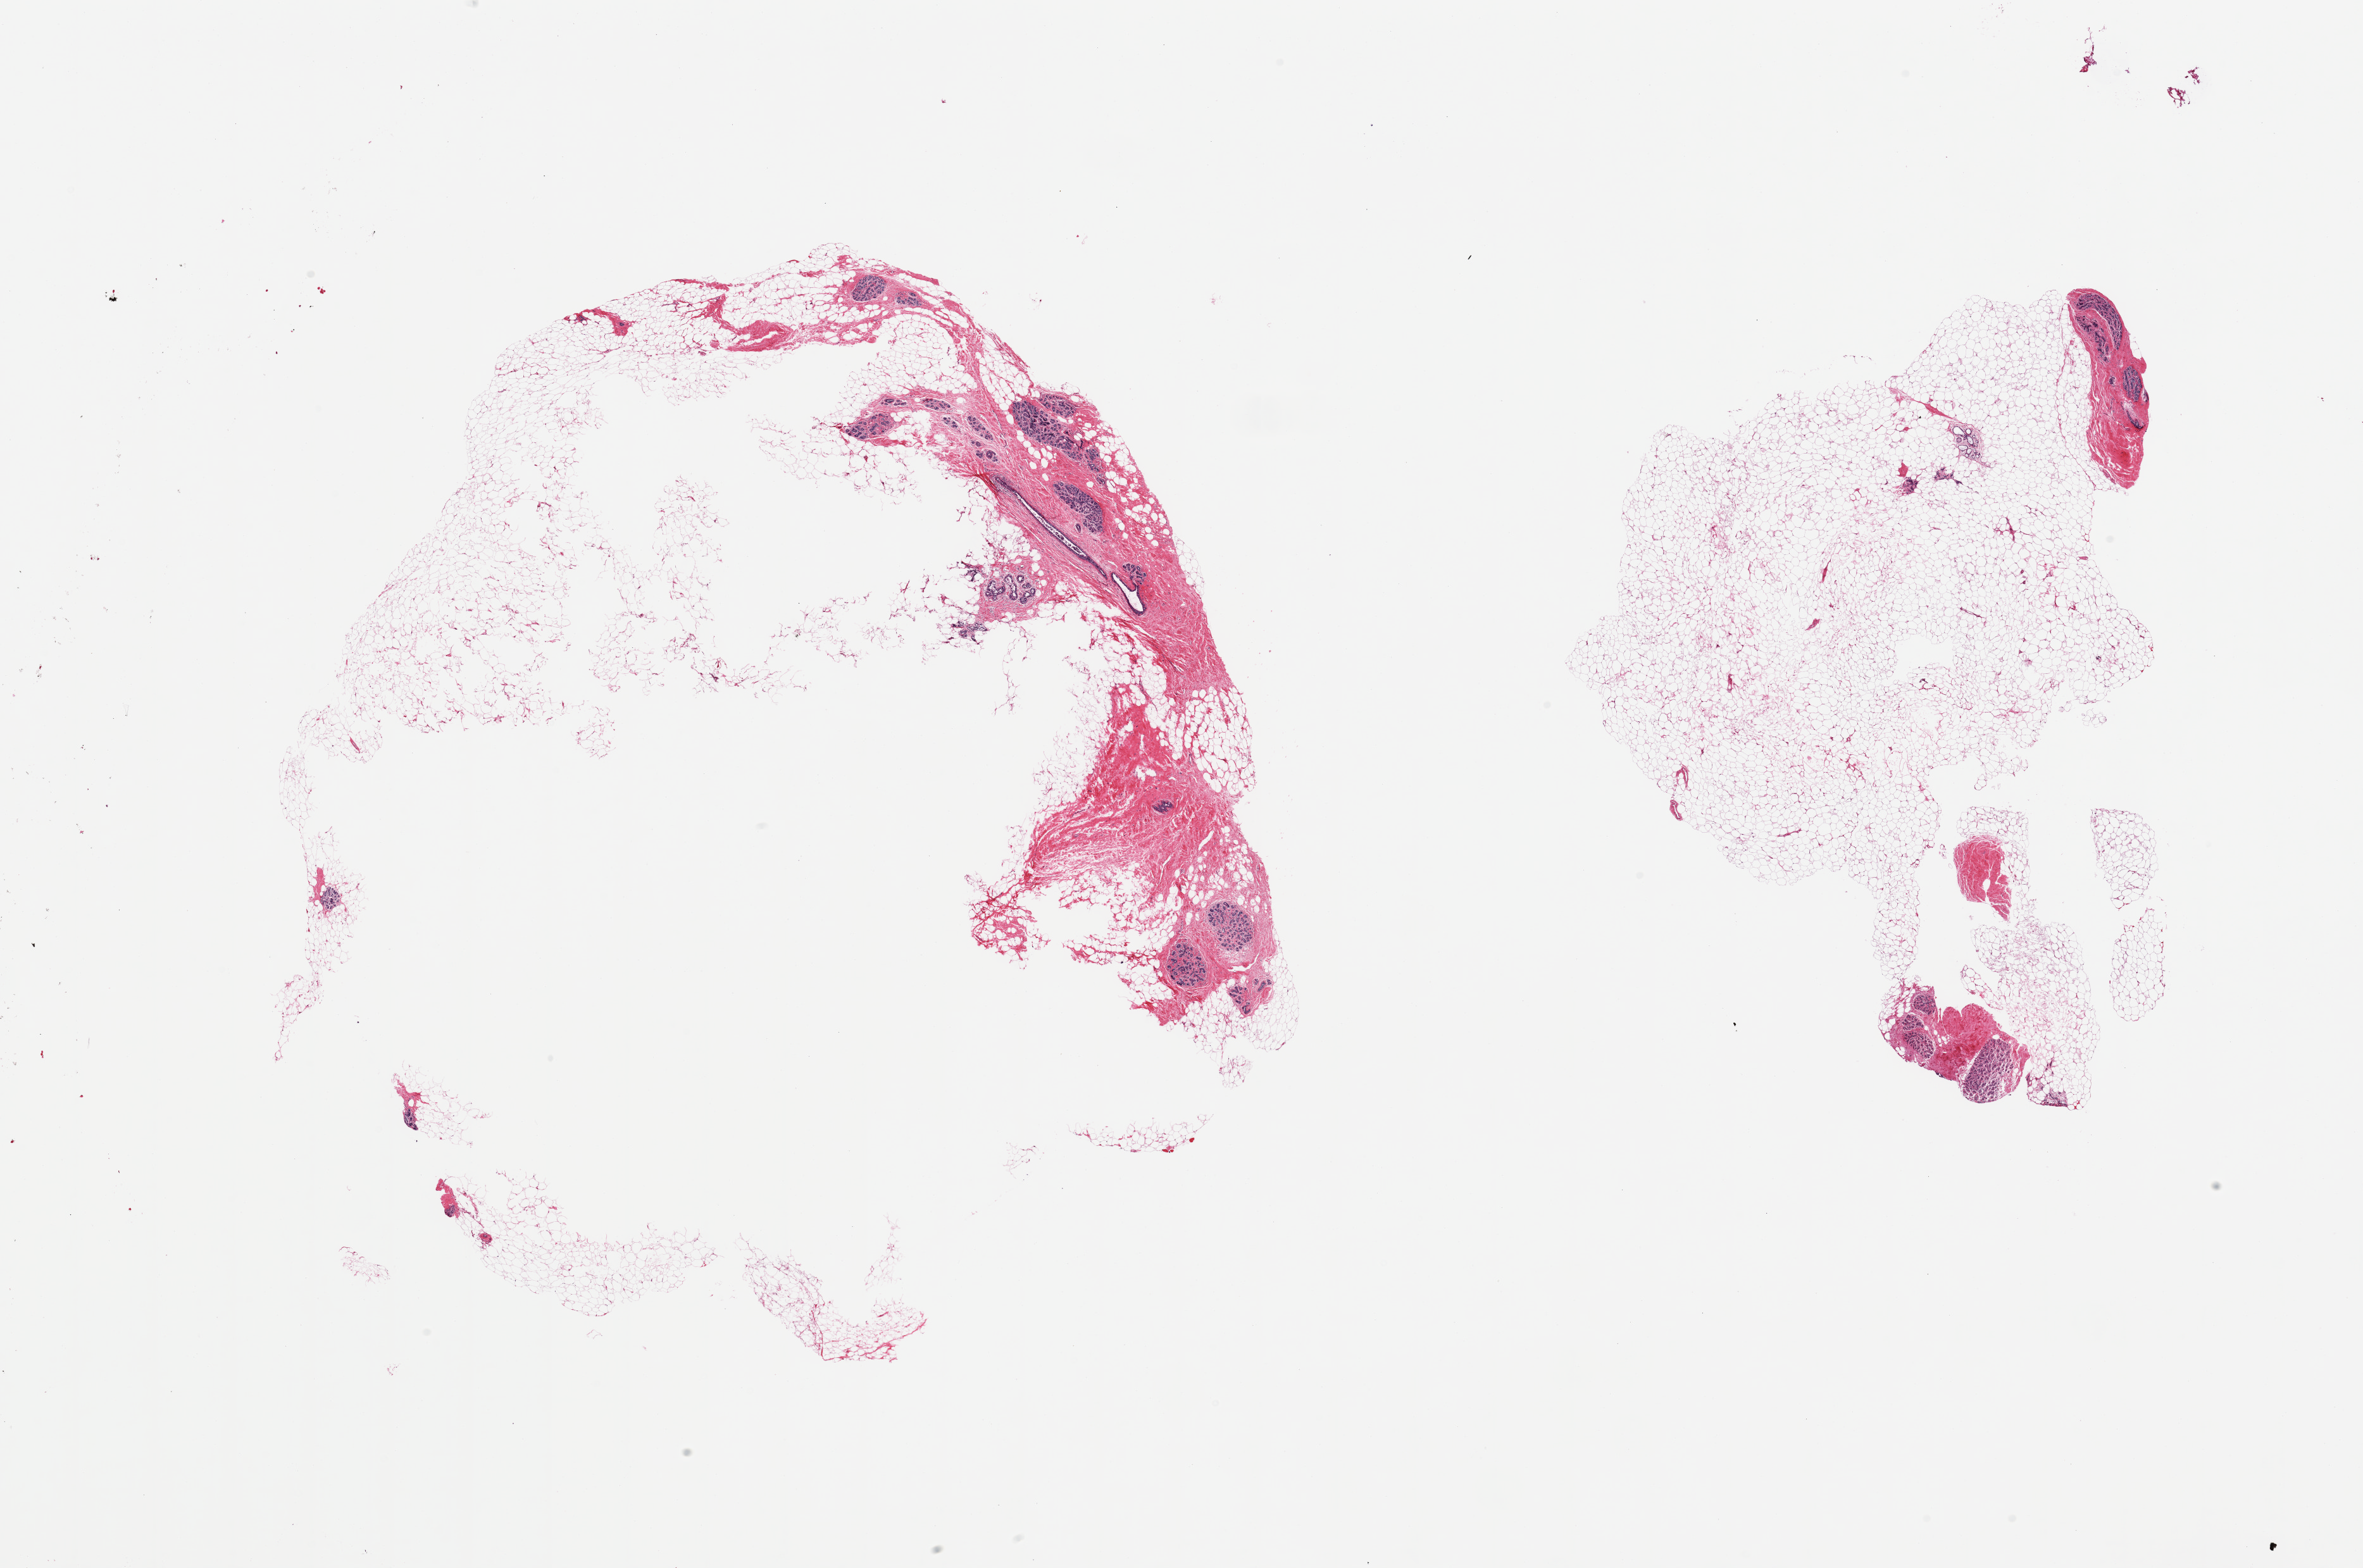
H&E whole-slide image — shown as a low-resolution overview of the whole scanned area (about 29.5 x 19.6 mm). PAXgene-fixed, paraffin-embedded tissue. Target tissue: breast. Donor tissue sample. Donor sex: female.
• review note (as recorded): 2 pieces, inactive ductal/lobular elements